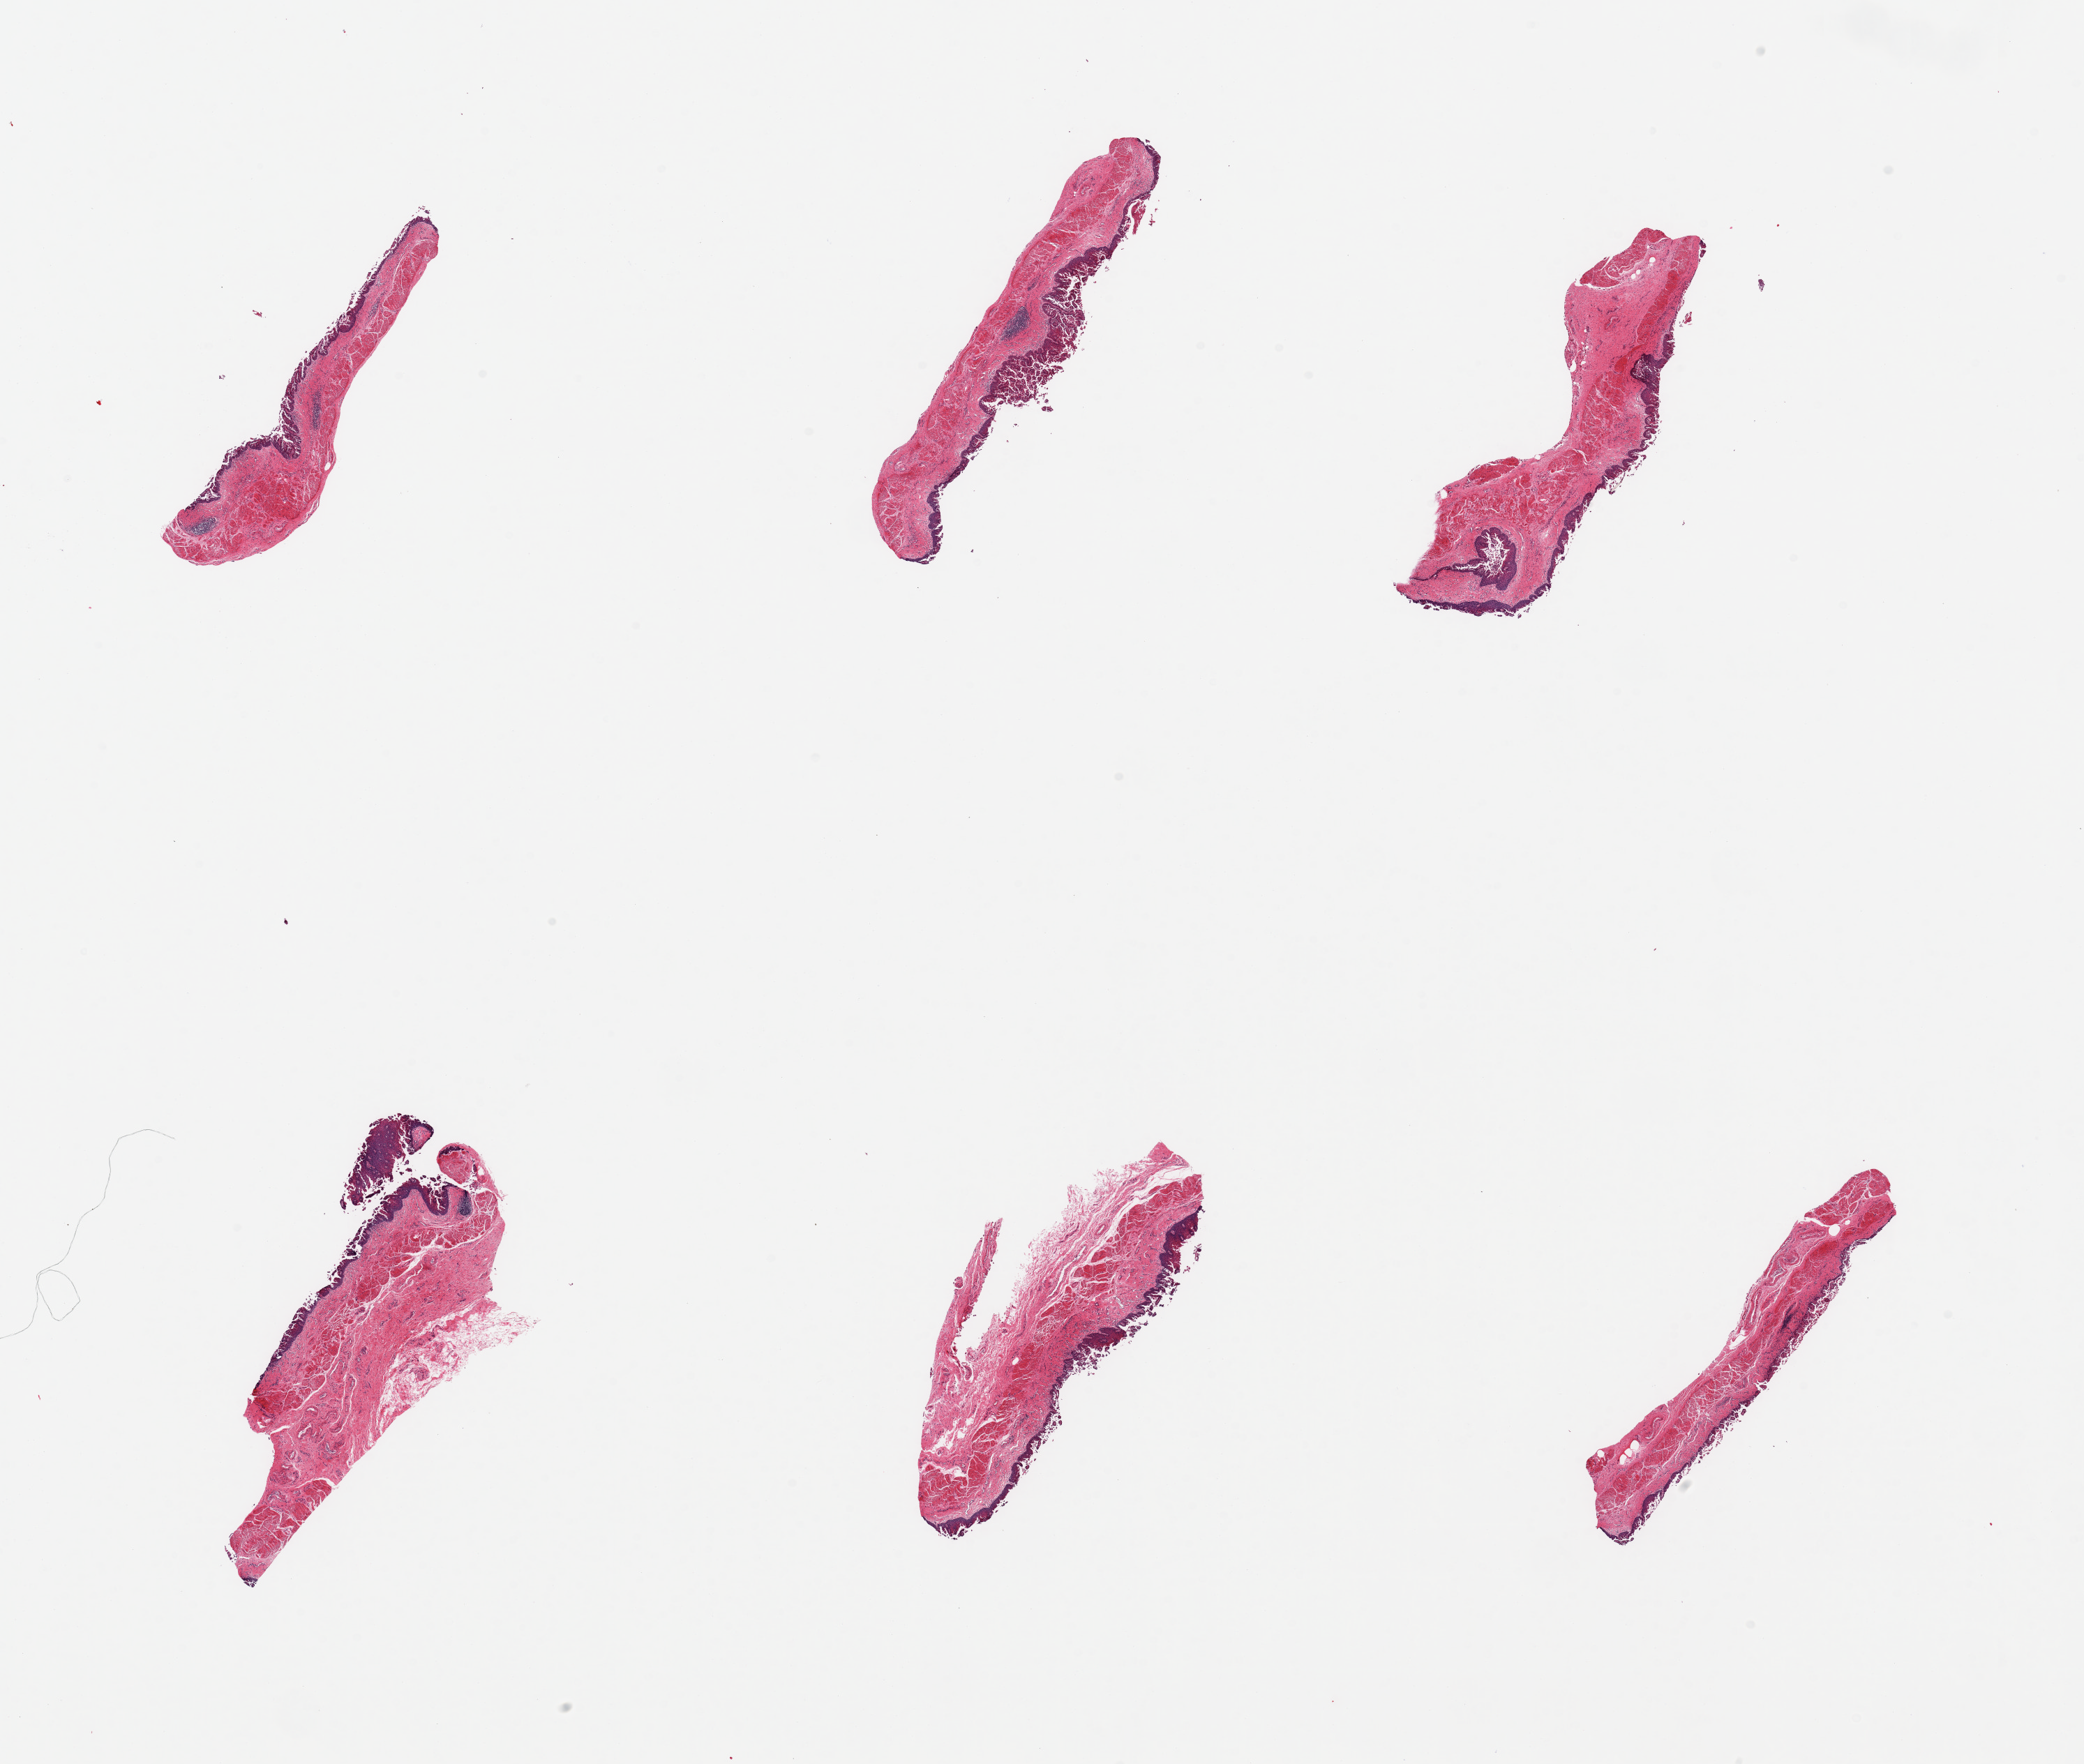
Whole-slide image, hematoxylin and eosin (H&E) stain, shown as a low-resolution overview of the whole scanned area (about 23.6 x 20.0 mm, acquisition: 20x scan); PAXgene-fixed, paraffin-embedded tissue; target tissue: esophageal mucous membrane; tissue donor sample. Donor sex: female.
Review note (as recorded): 6 pieces, squamous mucosa up to ~0.2mm, sloughing.